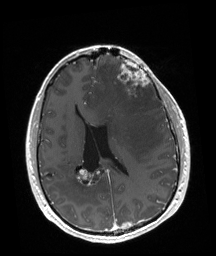
Brain MRI from a brain-tumour surgery series, one axial slice. Position 76 of 192 along the scan axis. T1-weighted post-contrast. 216 × 256 image matrix, field of view 219 × 260 mm.
Outlined on this slice (outlined manually by an expert reader):
- tumour: bounding box <118,59,150,98> (left, top, right, bottom; pixels)